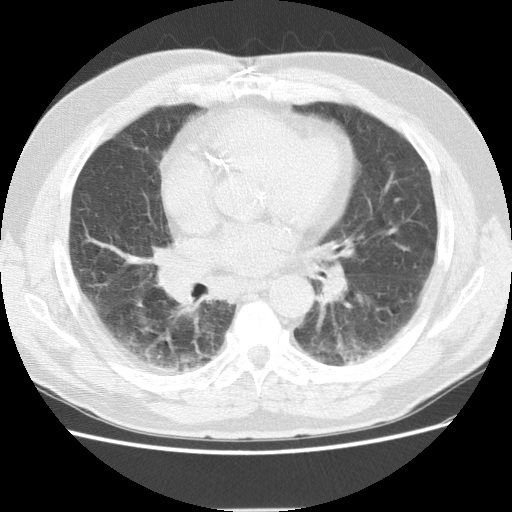
Axial slice from a low-dose chest CT screening exam, baseline screening round, lung window (W 1500 / L -600 HU). Male participant, aged 72 years at enrolment.
• Lesion marked by an expert reader, bounding box [x1, y1, x2, y2] px = [148, 237, 195, 274].
• No non-calcified nodule or mass ≥4 mm was recorded by the screening reader at this exam.
• Lung cancer was diagnosed 163 days after this screen: adenocarcinoma, NOS, right middle lobe, stage IIIB (AJCC 6th edition), 27 mm at pathology.